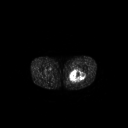
FDG PET of an extremity soft-tissue mass (from a PET/CT study), one axial slice; 128 × 128 image matrix. Patient: male, 44 years. Case-level facts recorded for this patient, not image findings: histological type: undifferentiated pleomorphic liposarcoma; grade: high; site of the primary tumour: left thigh.
Structures marked on this image (expert contour drawn on MRI and transferred to this co-registered scan by the dataset authors):
- gross tumour volume including surrounding oedema: bounding box [x1, y1, x2, y2] px = [68, 69, 85, 83]
- gross tumour volume (mass): [70, 70, 85, 81]